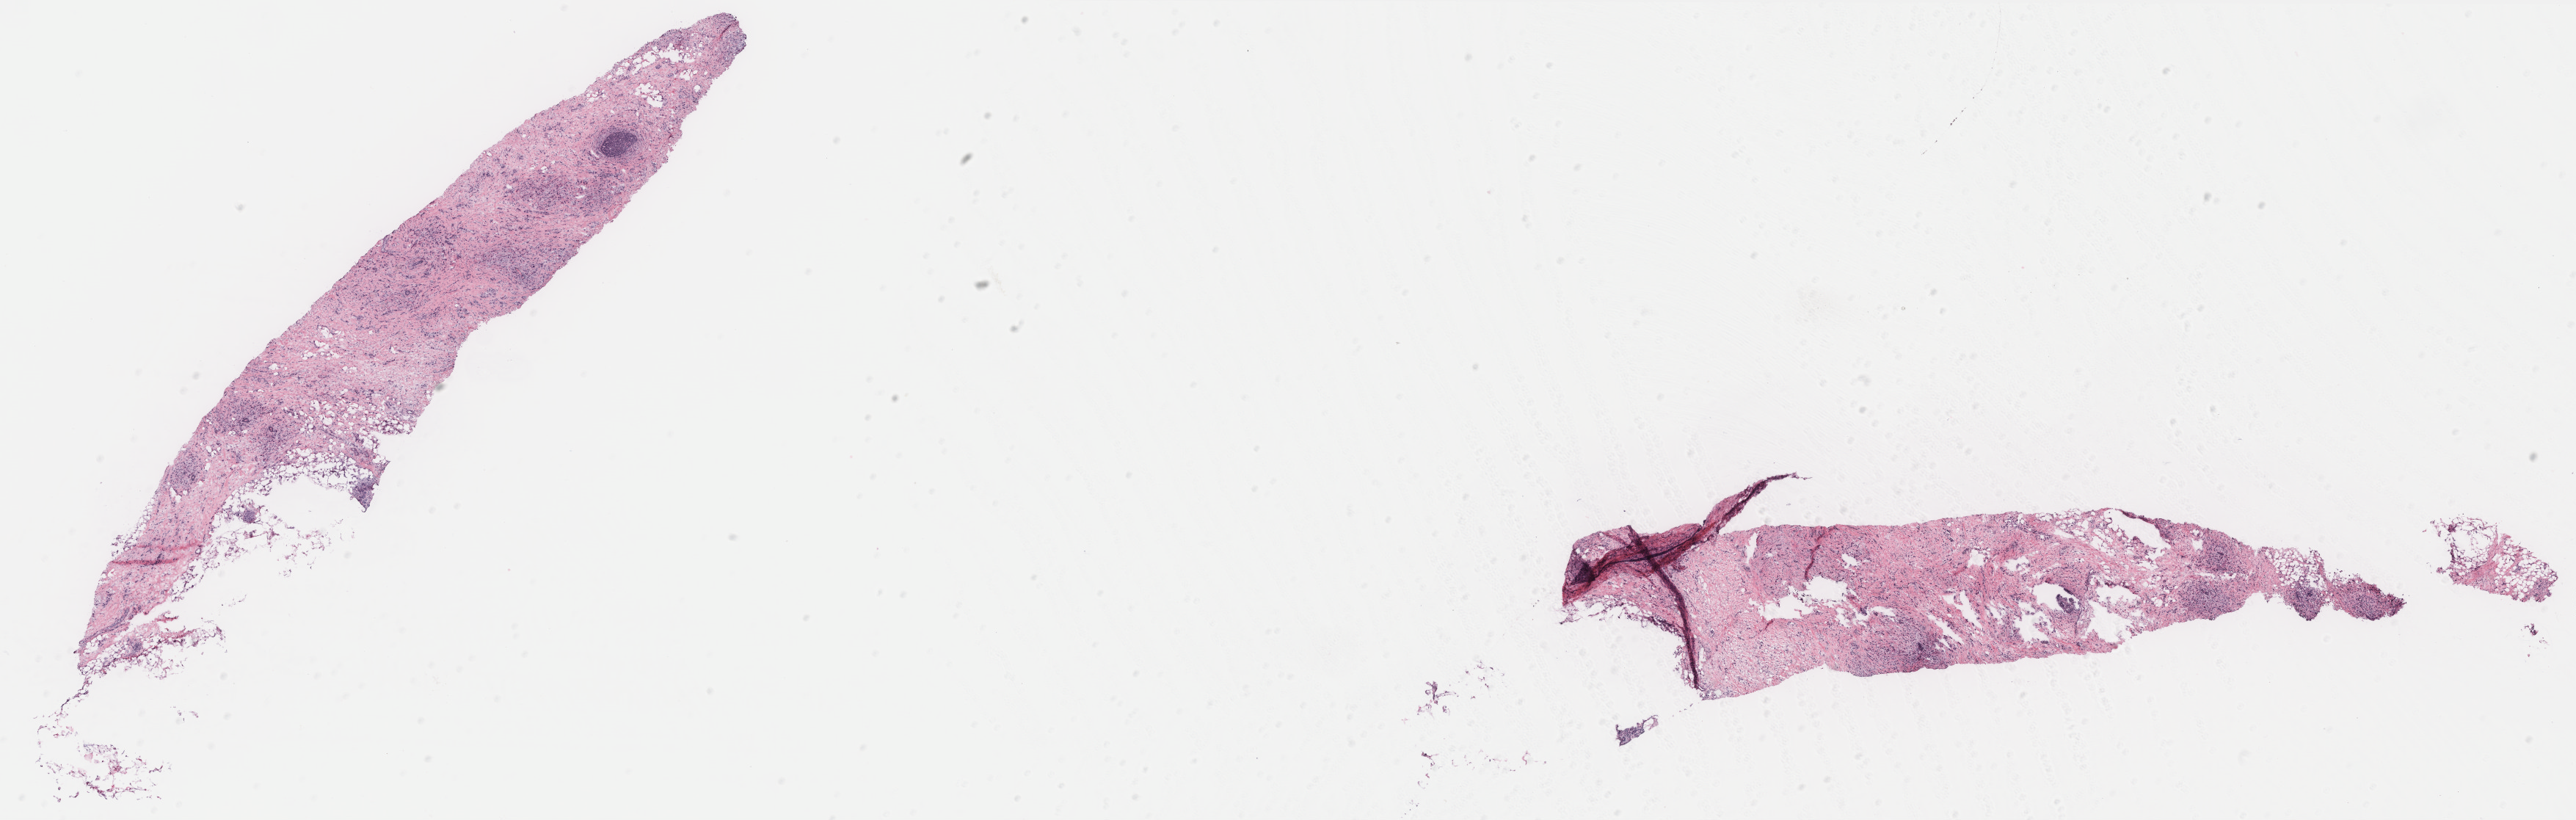
Whole-slide histology image, H&E — a low-resolution overview of the entire scanned area, about 28.1 x 8.9 mm. Breast, tissue type not recorded. 50-year-old female patient.
Patient diagnosis: Infiltrating duct carcinoma, NOS.